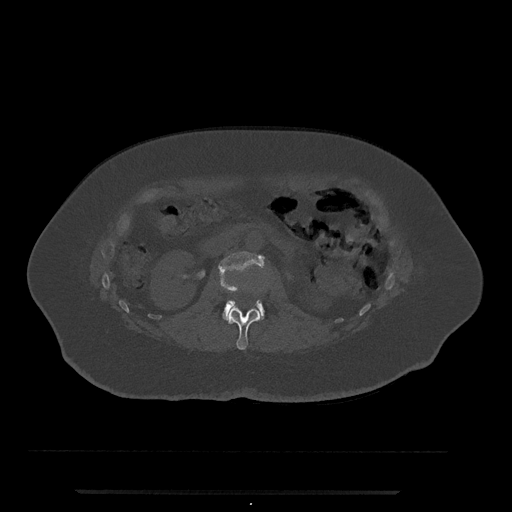
CT including the spine, one axial slice; slice 70 of 797 in the series (ordered by position); reconstruction kernel Br40s/3; 120 kVp; bone window (W 1800 / L 400 HU); 512 × 512 image matrix, field of view 440 × 440 mm. Female patient, age 51 years. Case-level facts recorded for this patient, not image findings: primary cancer: neuro.
Annotated regions visible in this slice (semi-automatic segmentation, software-assisted and operator-edited):
- L1 vertebra: bounding box (x1, y1, x2, y2) in pixels: (224, 308, 262, 350)
- L2 vertebra: (219, 251, 265, 320)